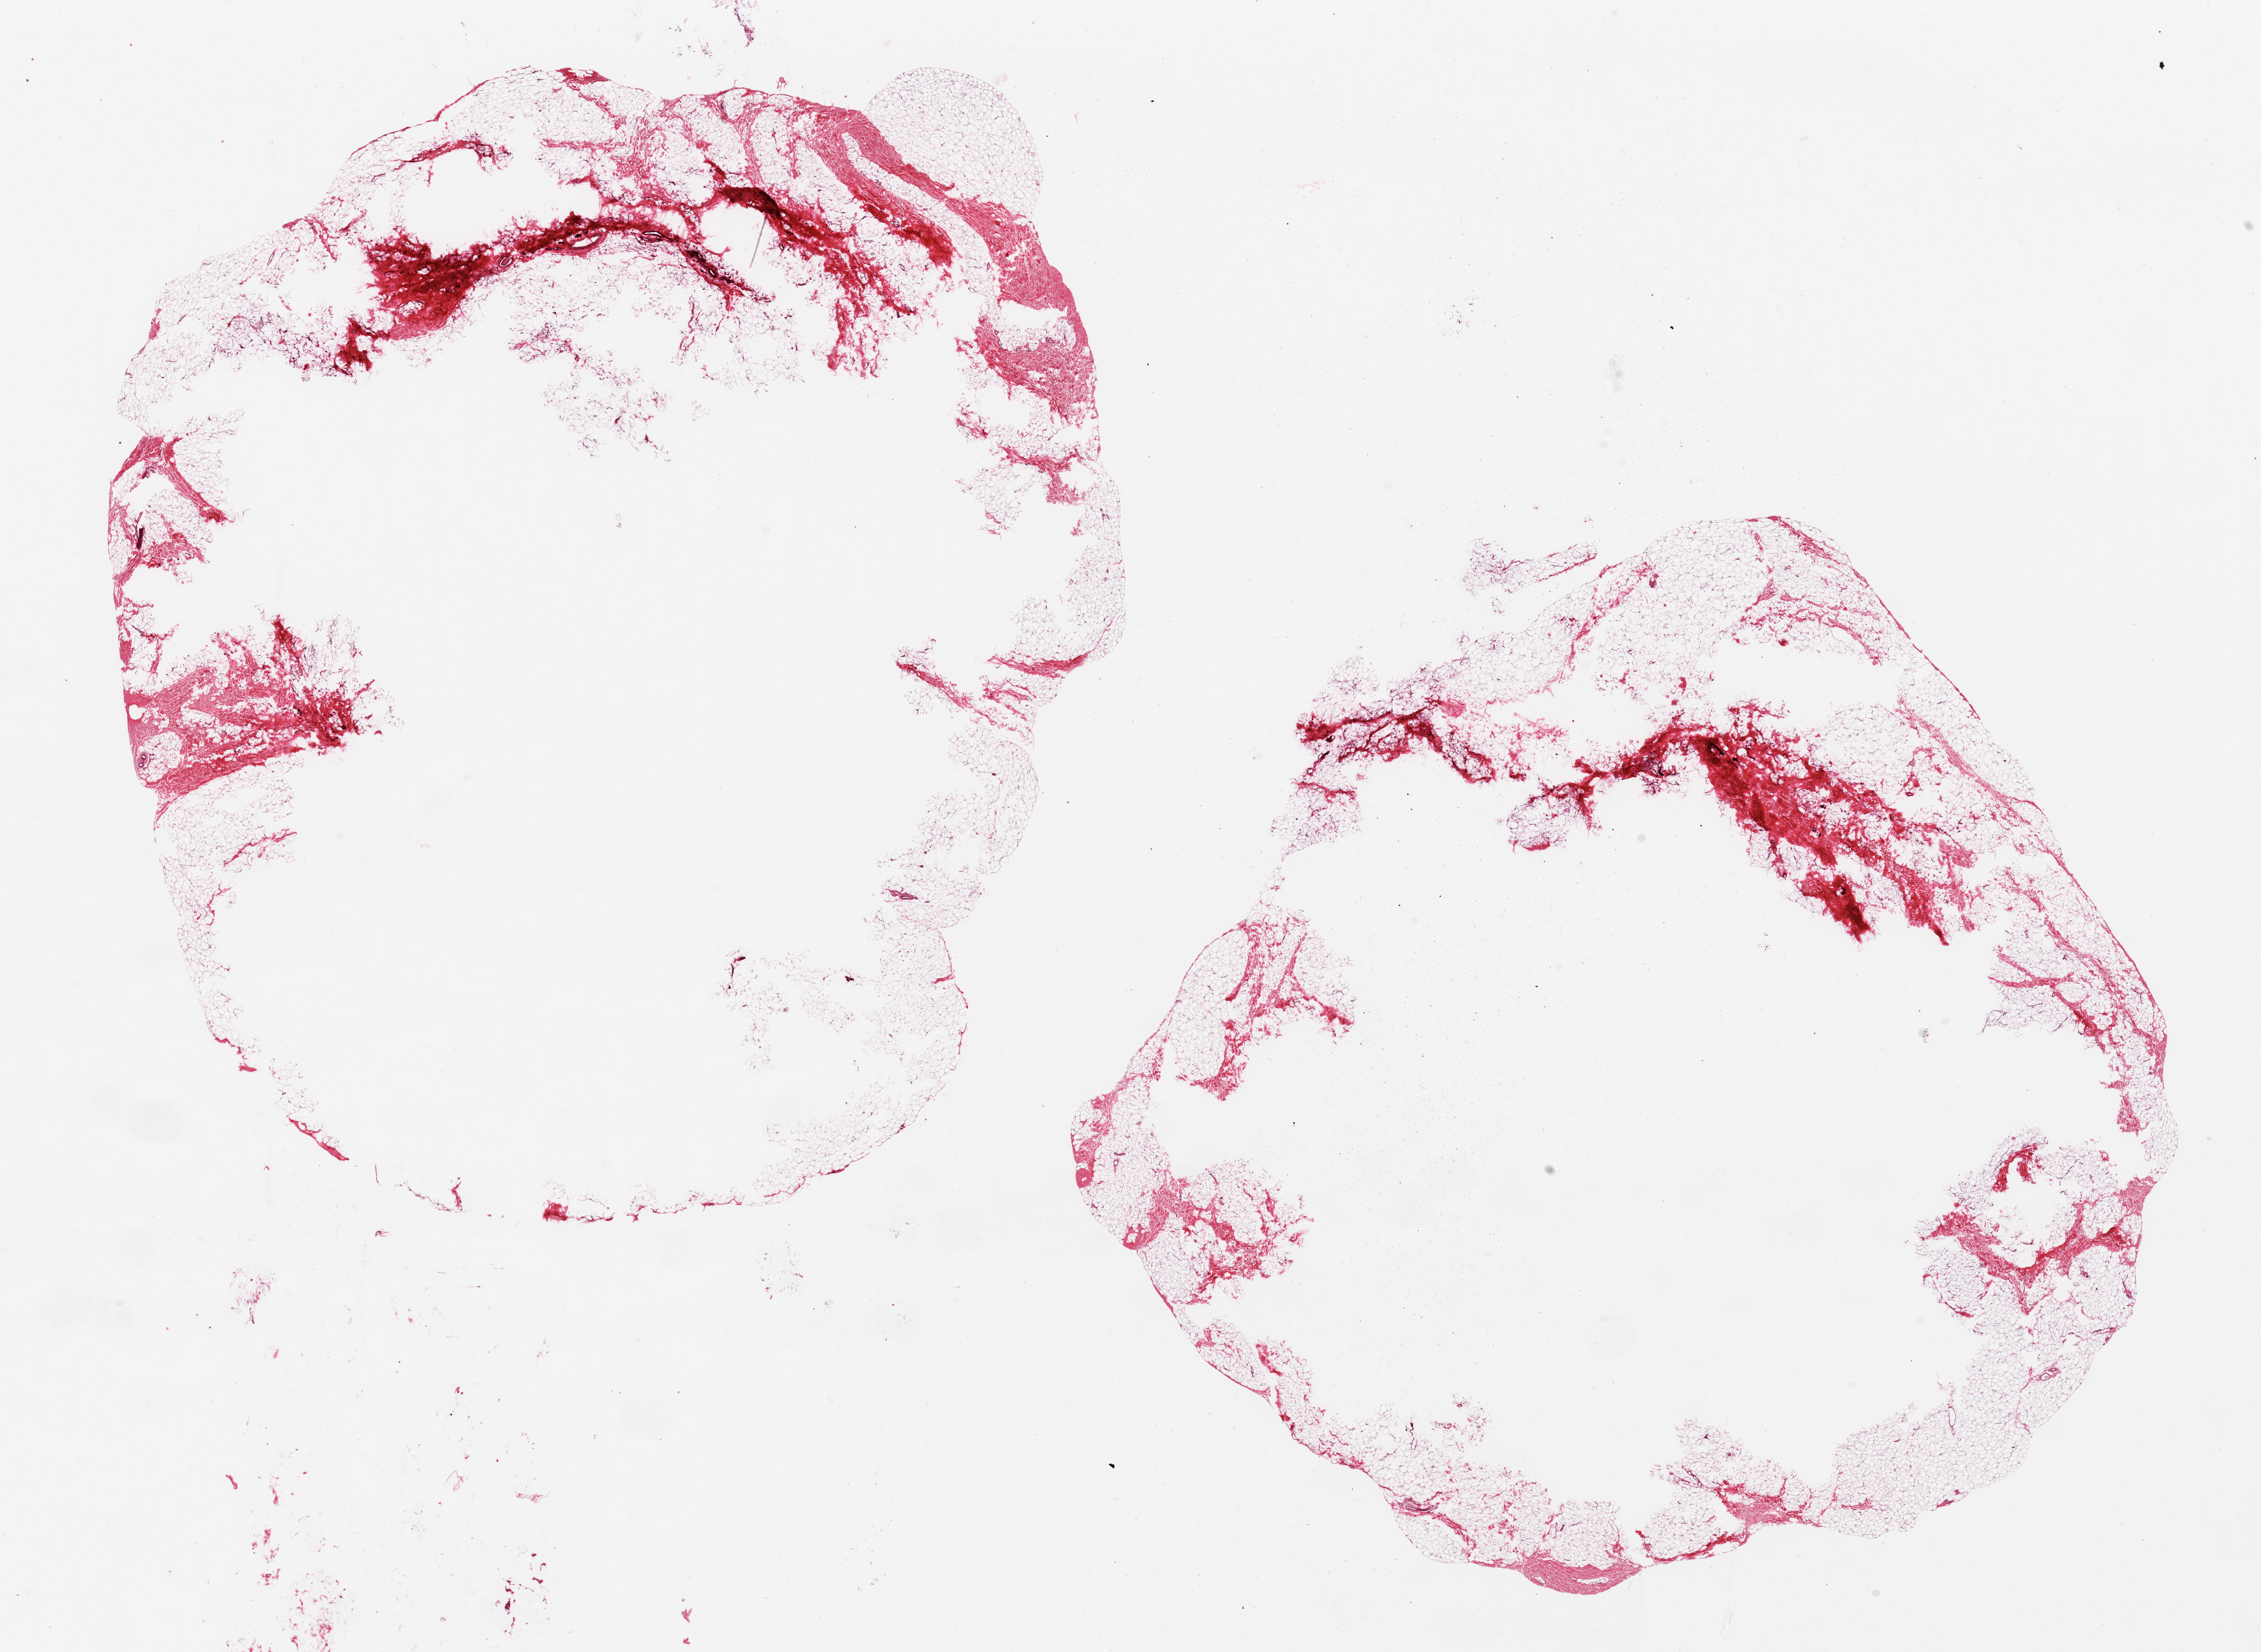
Haematoxylin and eosin whole-slide image — low-resolution overview of the scanned area, about 27.6 x 20.1 mm. PAXgene-fixed paraffin-embedded (PFPE) section. Target tissue: breast. Tissue donor sample. Donor: male.
- reviewer comment on this tissue sample: 2 pieces of adipose tissue without mammary elements; large central defects in 15x12 & 12x12 mm aliquots; probably poorly fixed